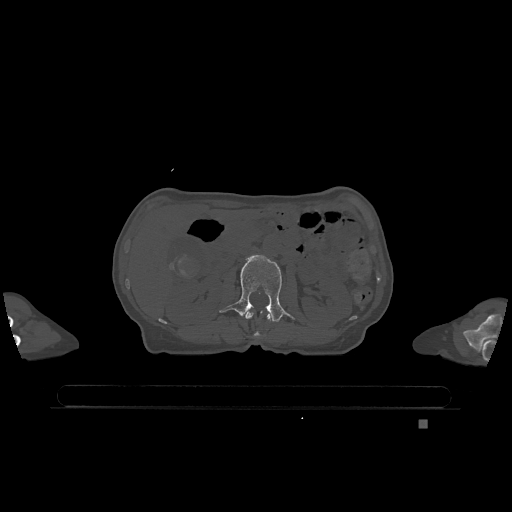
CT including the spine, one axial slice. Bone window (W 1800 / L 400 HU). 0.5 mm slice thickness. 512 × 512 image matrix, field of view 500 × 500 mm. Patient: female, 74 years. From the clinical record (not read from this slice): primary cancer: lung; vertebrae with lytic lesions (as recorded): T1, T4, T5, T6, L4, L5.
Structures marked on this image (semi-automatic segmentation, software-assisted and operator-edited):
- L1 vertebra: box from (x=243, y=311) to (x=271, y=338) px
- L2 vertebra: (x=219, y=255)–(x=294, y=322)